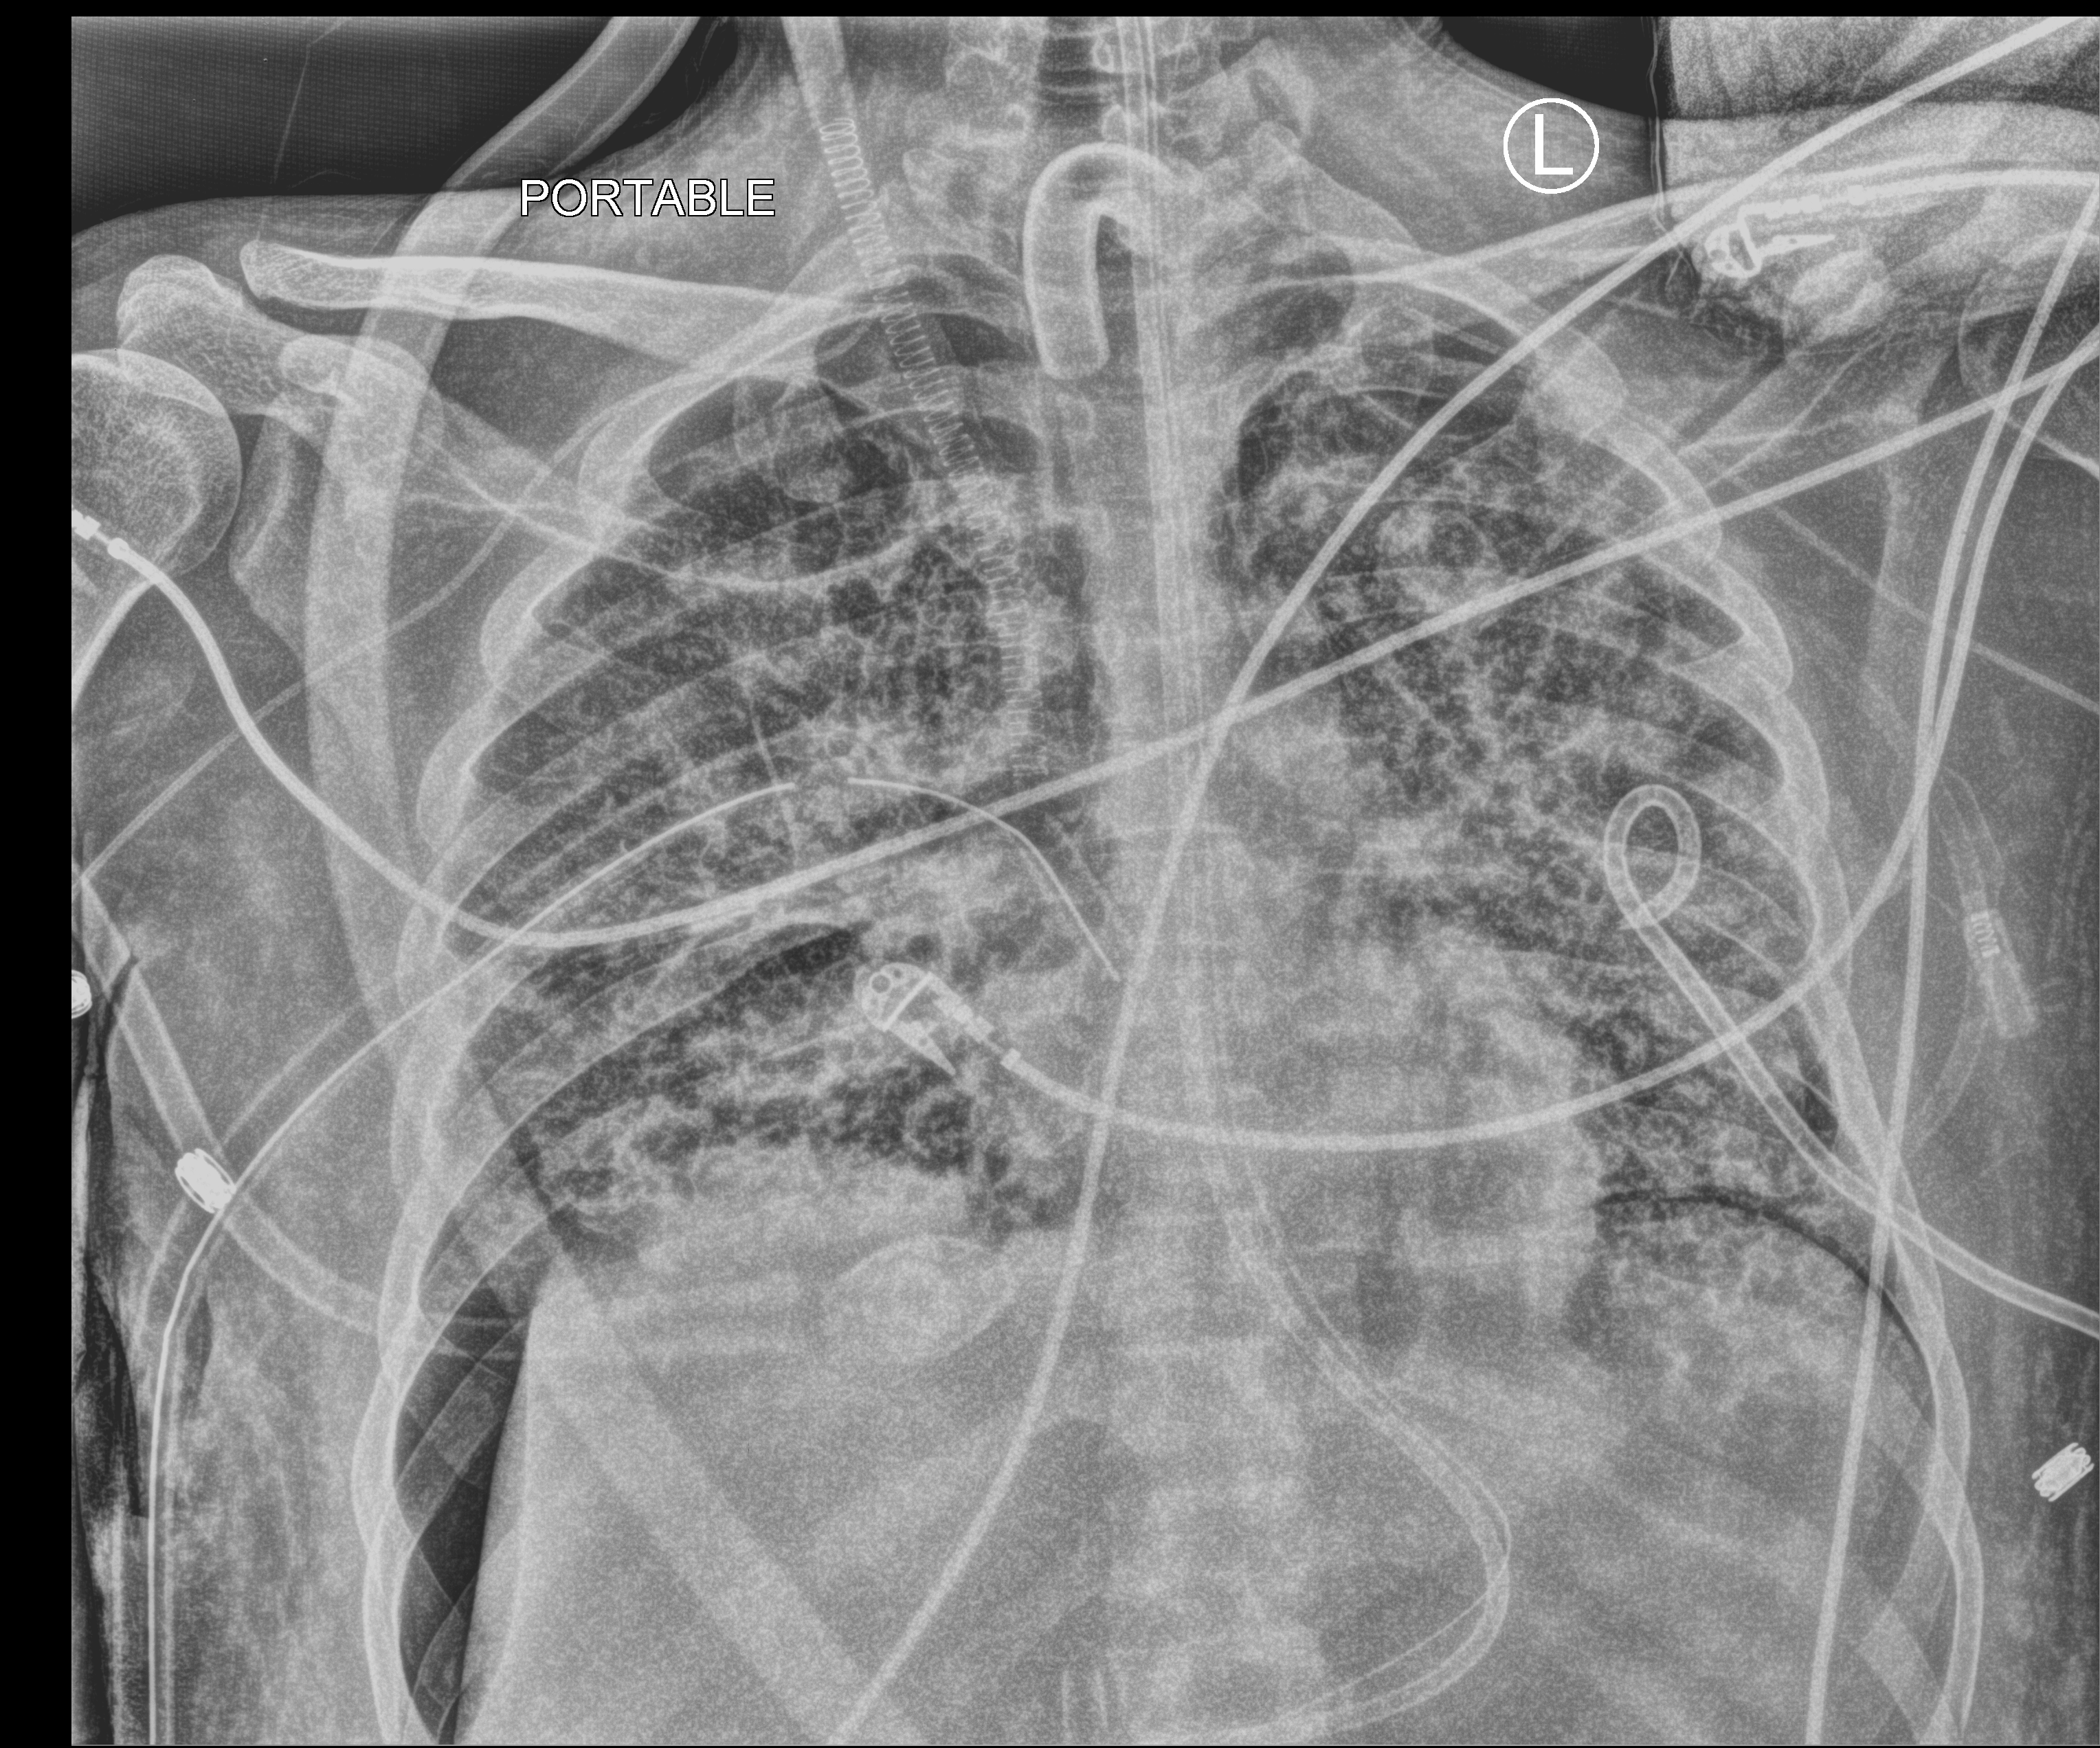
Chest X-ray (portable); anteroposterior (AP) projection. Patient hospitalised with COVID-19, aged 18–59 years.
Admission-level facts for this patient (not findings on this image; timing relative to this image not recorded): admitted to intensive care during this hospital stay: yes.